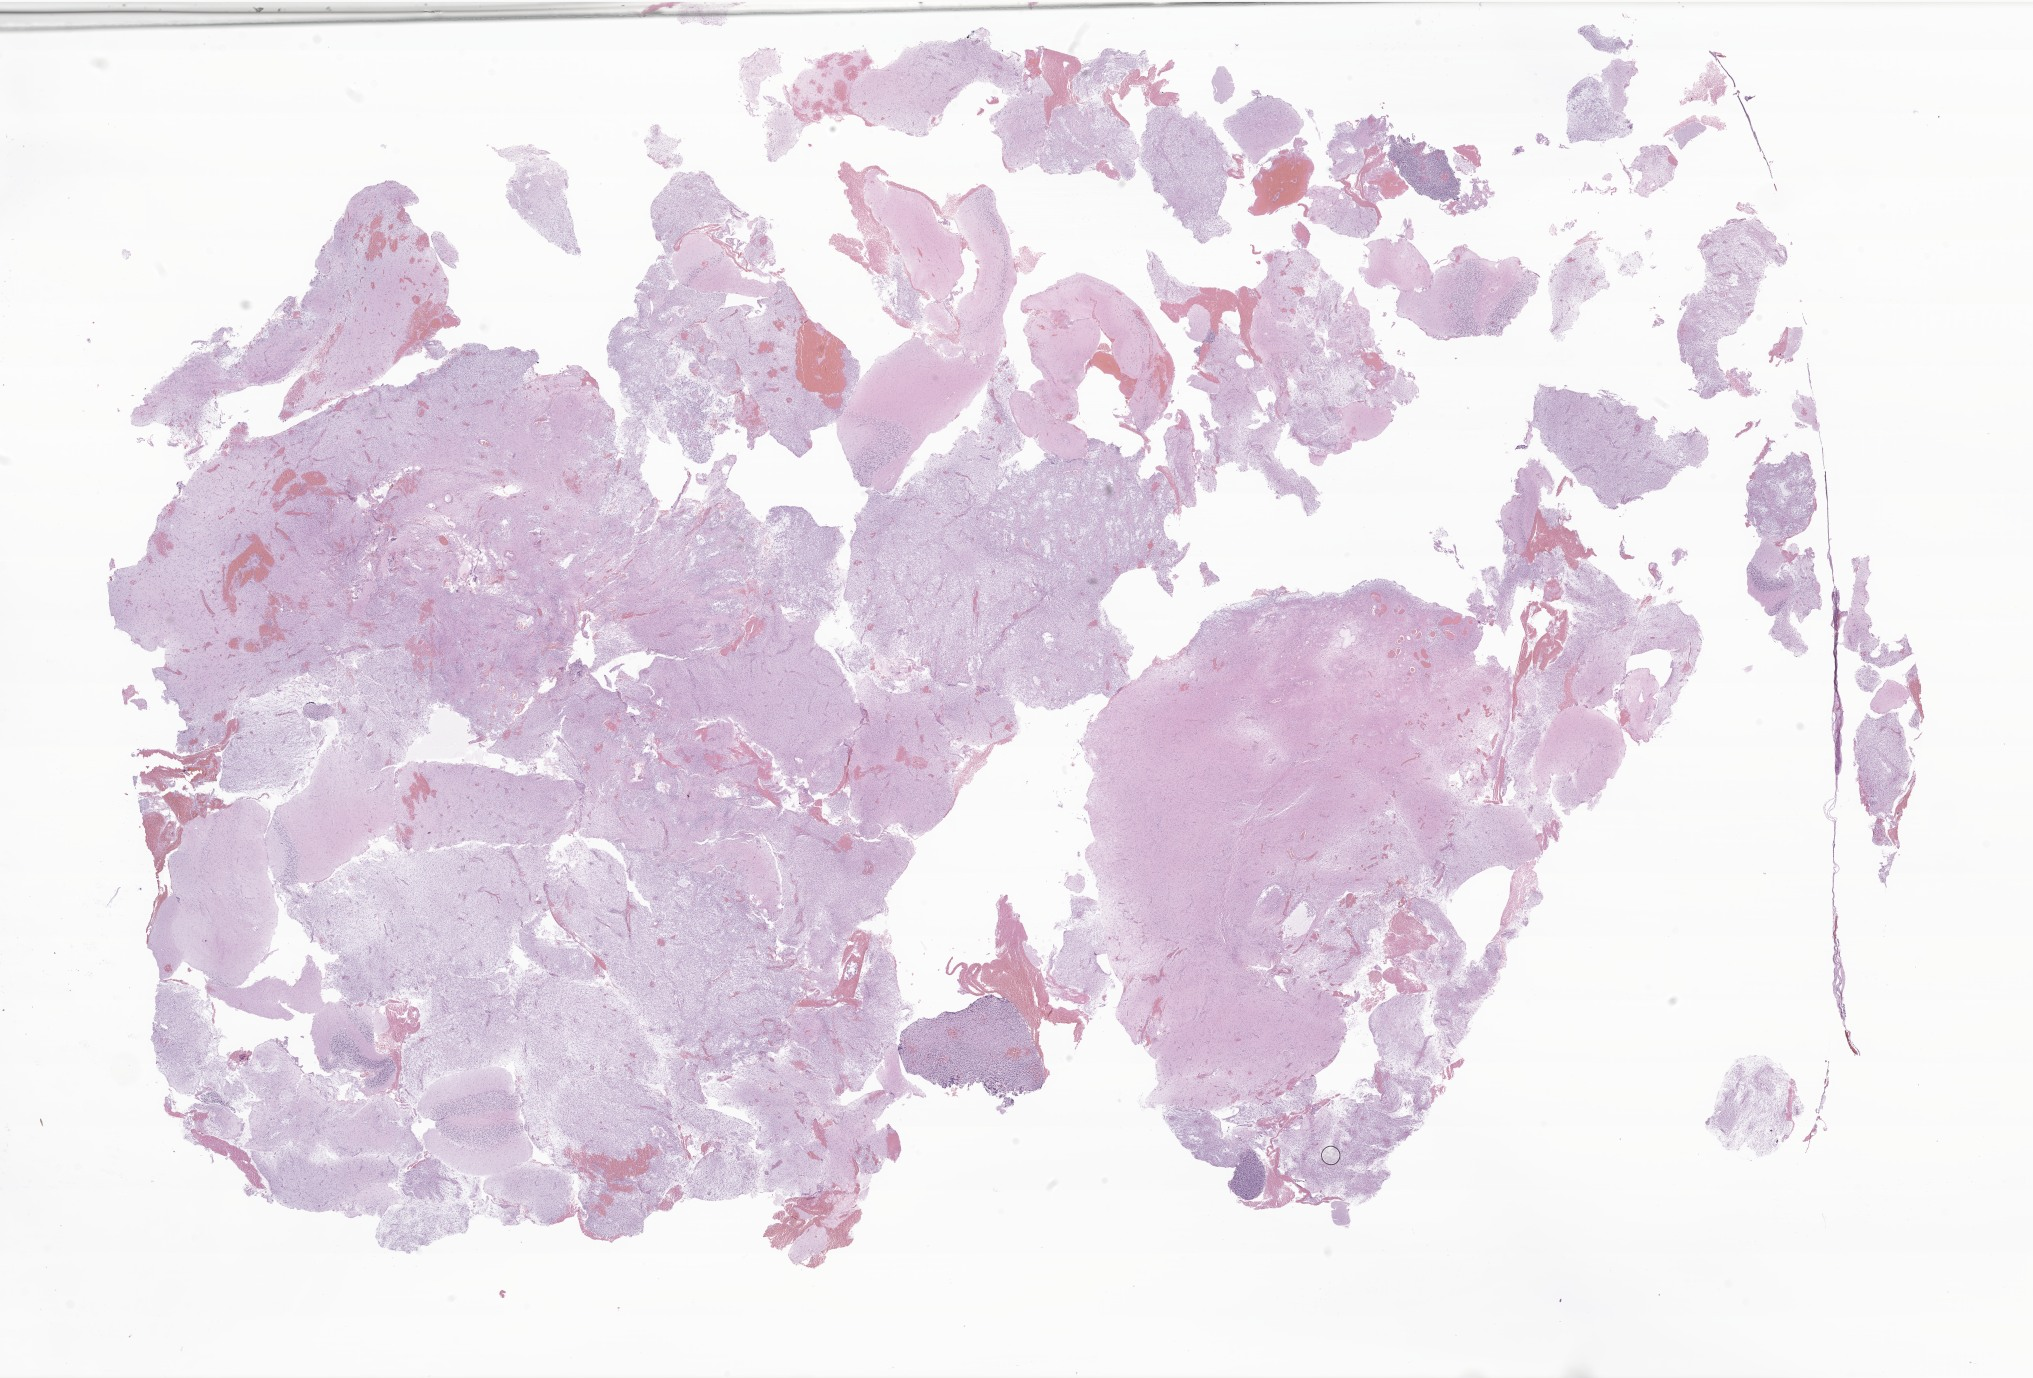
Digitized H&E-stained section of tumor tissue from the brain, low-resolution overview of the scanned area, about 34.3 x 23.2 mm. Formalin-fixed, paraffin-embedded (FFPE) tissue. Male patient, age 52 months (4 years 4 months).
- diagnosis (ICD-O-3 morphology term): Pilocytic astrocytoma